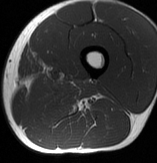
MRI of an extremity soft-tissue mass, one axial slice. Slice 21 of 70 in the series (ordered by position). MR volume resampled by the dataset authors to the PET/CT grid (not the native acquisition matrix). 3.27 mm slice thickness. 157 × 163 image matrix, field of view 153 × 159 mm. Male patient. From the clinical record (not read from this slice): histological type: extraskeletal osteosarcoma; grade: high; site of the primary tumour: left adductur.
Annotated regions visible in this slice (expert contour drawn on MRI and transferred to this co-registered scan by the dataset authors):
- gross tumour volume (mass): bounding box (x1, y1, x2, y2) in pixels: (28, 76, 98, 105)